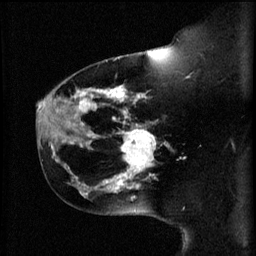
Breast MRI (dynamic contrast-enhanced), one sagittal slice. Slice 42 of 60 in the series (ordered by position). 3 images stored at this slice position (order not interpretable as contrast timing). 1.5 T. TE 4.2 ms, TR 11 ms. 256 × 256 image matrix, field of view 180 × 180 mm. Female patient, age 44 years.
Annotated regions visible in this slice (semi-automatic segmentation, software-assisted and operator-edited):
- analysis volume of interest (the breast-tissue region the enhancement analysis was run in; not a lesion): bounding box (x1, y1, x2, y2) in pixels: (112, 124, 159, 179)
- tumour enhancement mask (voxels above the 70 % enhancement threshold inside the analysis volume of interest): (112, 130, 157, 179)